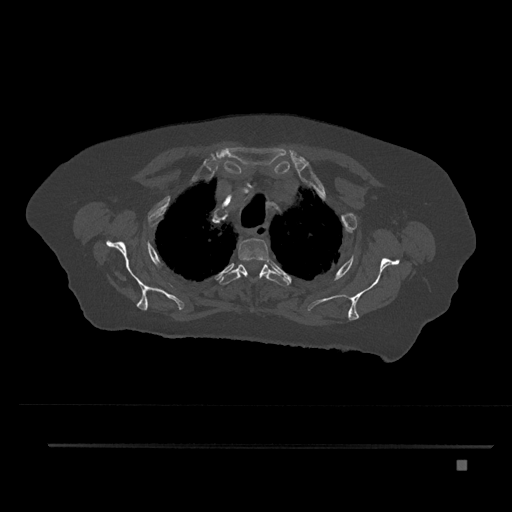
CT including the spine, one axial slice. Position 649 of 797 along the scan axis. Reconstruction kernel Br40s/3. 120 kVp. Bone window (W 1800 / L 400 HU). 0.5 mm slice thickness. 512 × 512 image matrix, field of view 437 × 437 mm. Patient: female, 76 years. Case-level facts recorded for this patient, not image findings: primary cancer: lung; vertebrae with lytic lesions (as recorded): T11, L3.
Annotated regions visible in this slice (semi-automatic segmentation, software-assisted and operator-edited):
- T2 vertebra: bounding box <238,238,271,272> (left, top, right, bottom; pixels)
- T3 vertebra: <219,261,289,286>